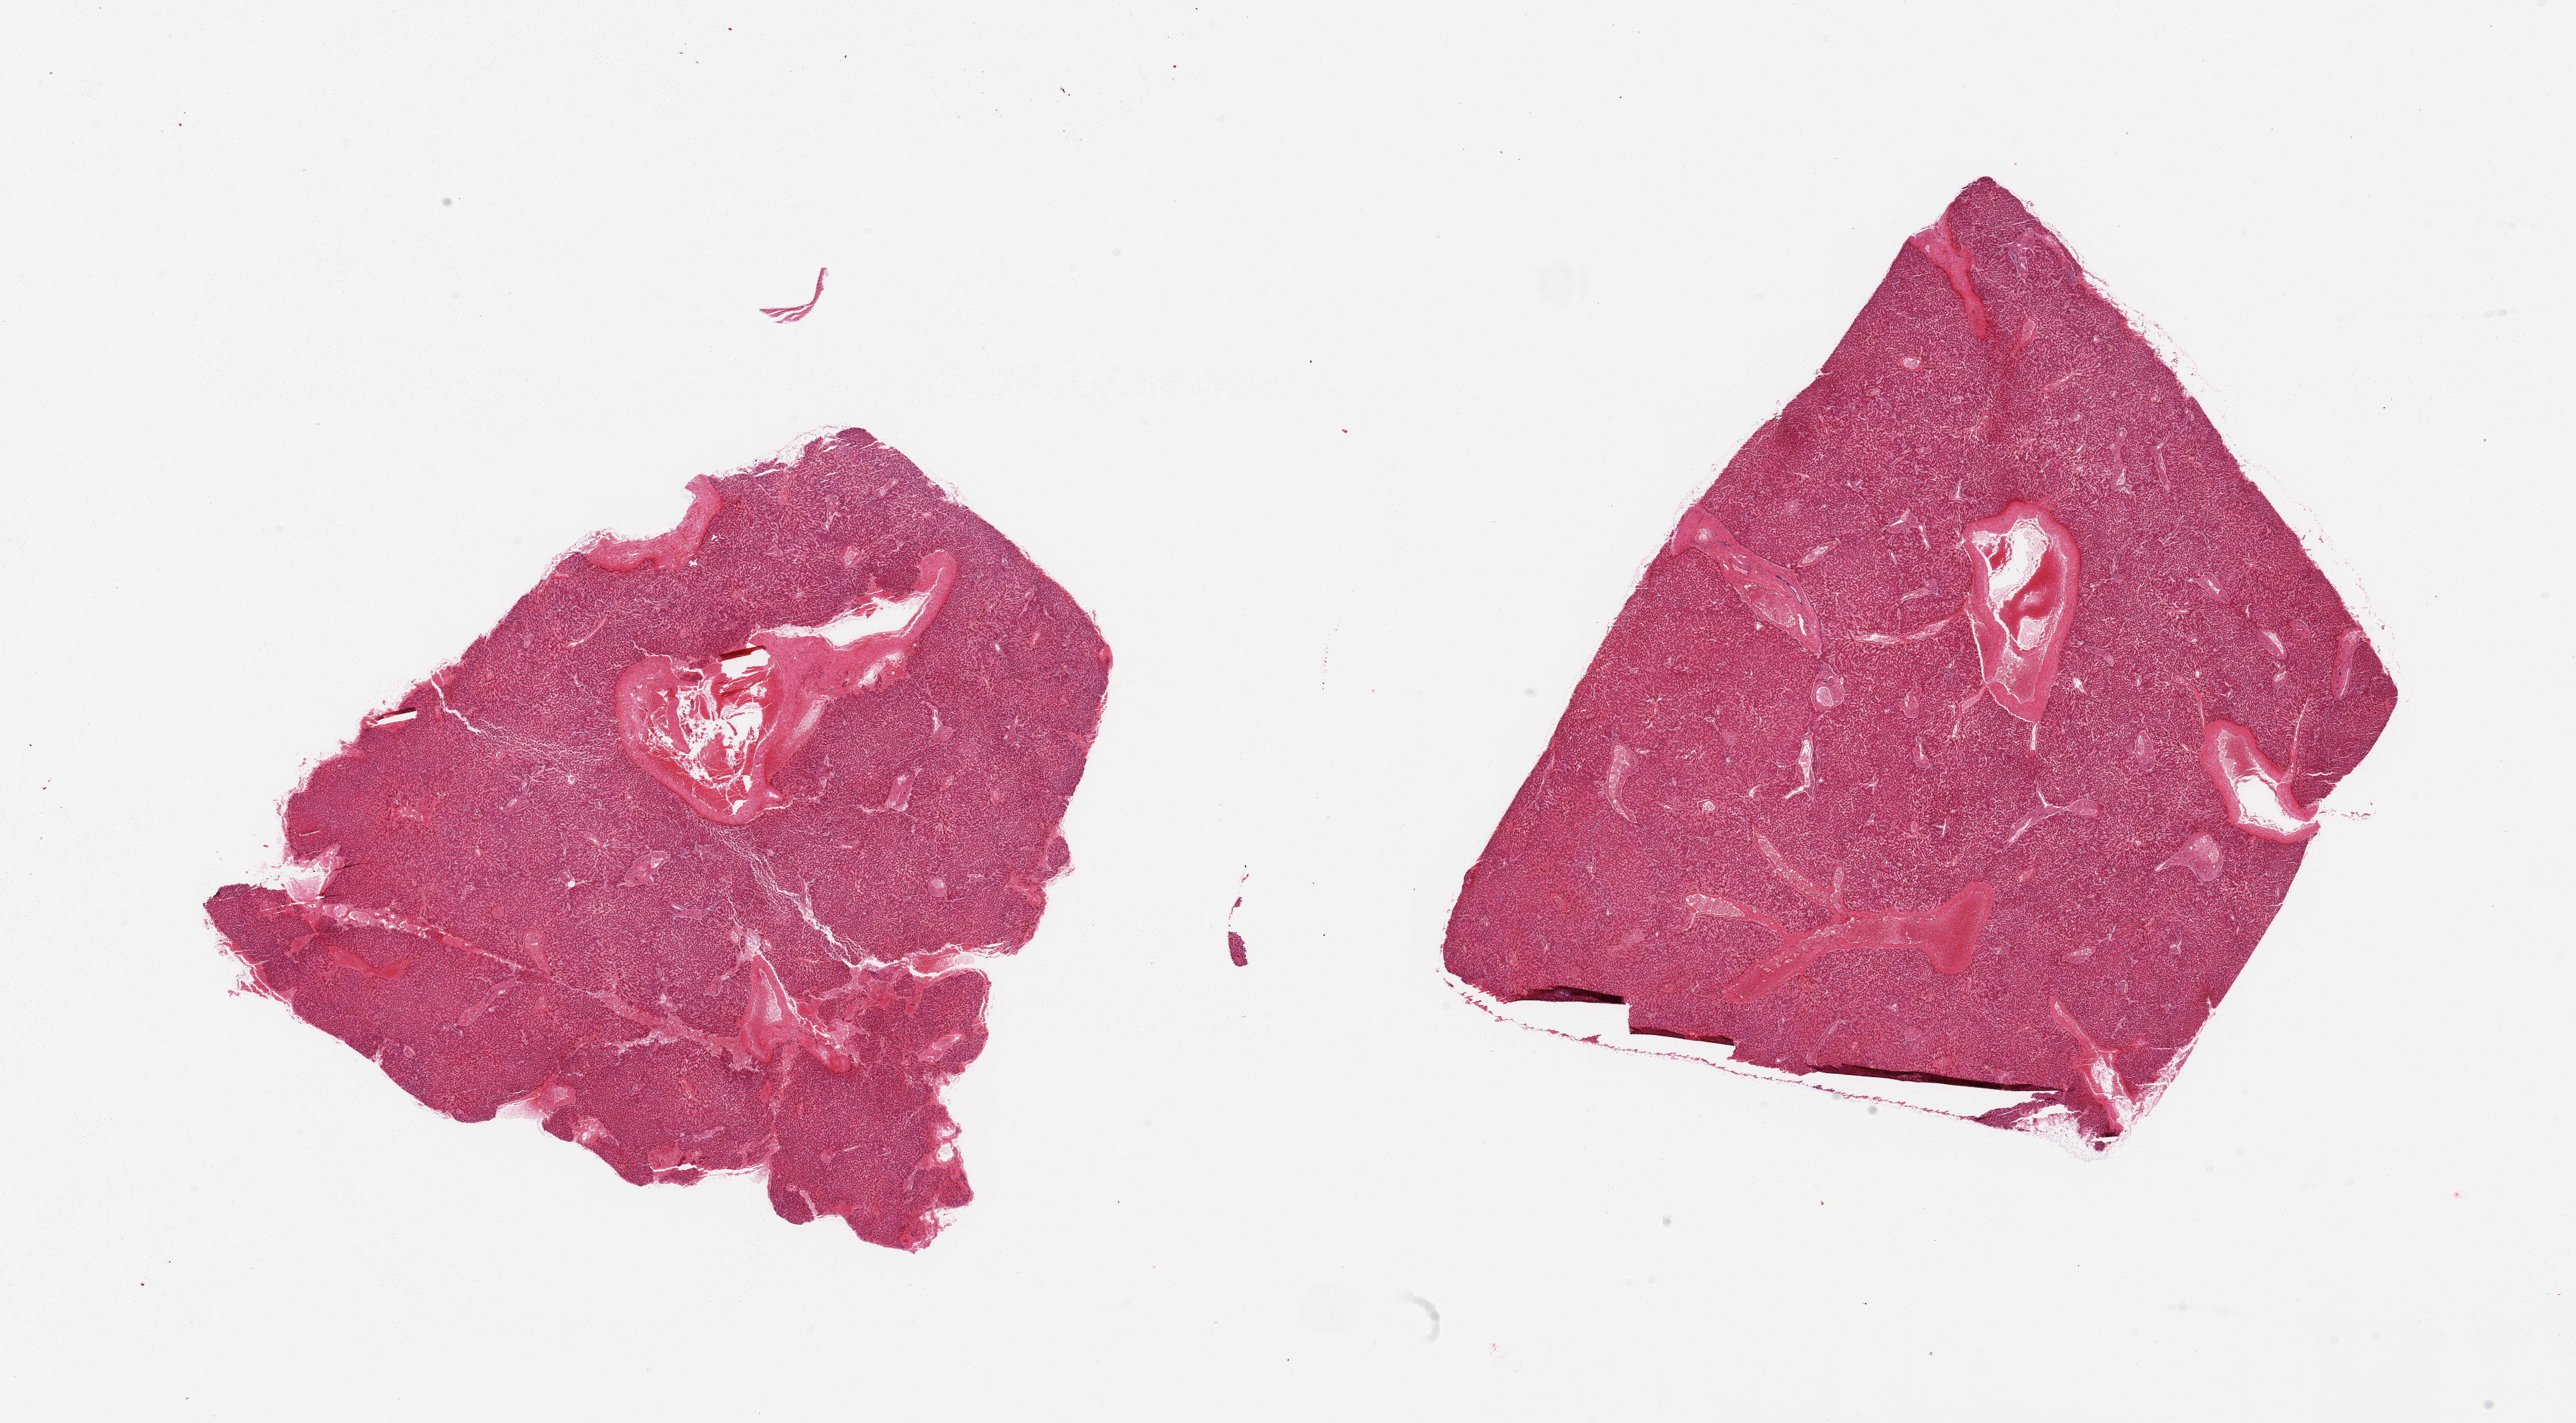
Whole-slide image, haematoxylin and eosin stain, shown as a low-resolution overview of the whole scanned area (about 30.5 x 16.9 mm, acquisition: 20x scan), PAXgene-fixed paraffin-embedded (PFPE) section, section of liver (target tissue), donor tissue sample. Male donor.
Pathologist's review note for this sample: 2 pieces; marked congestion.